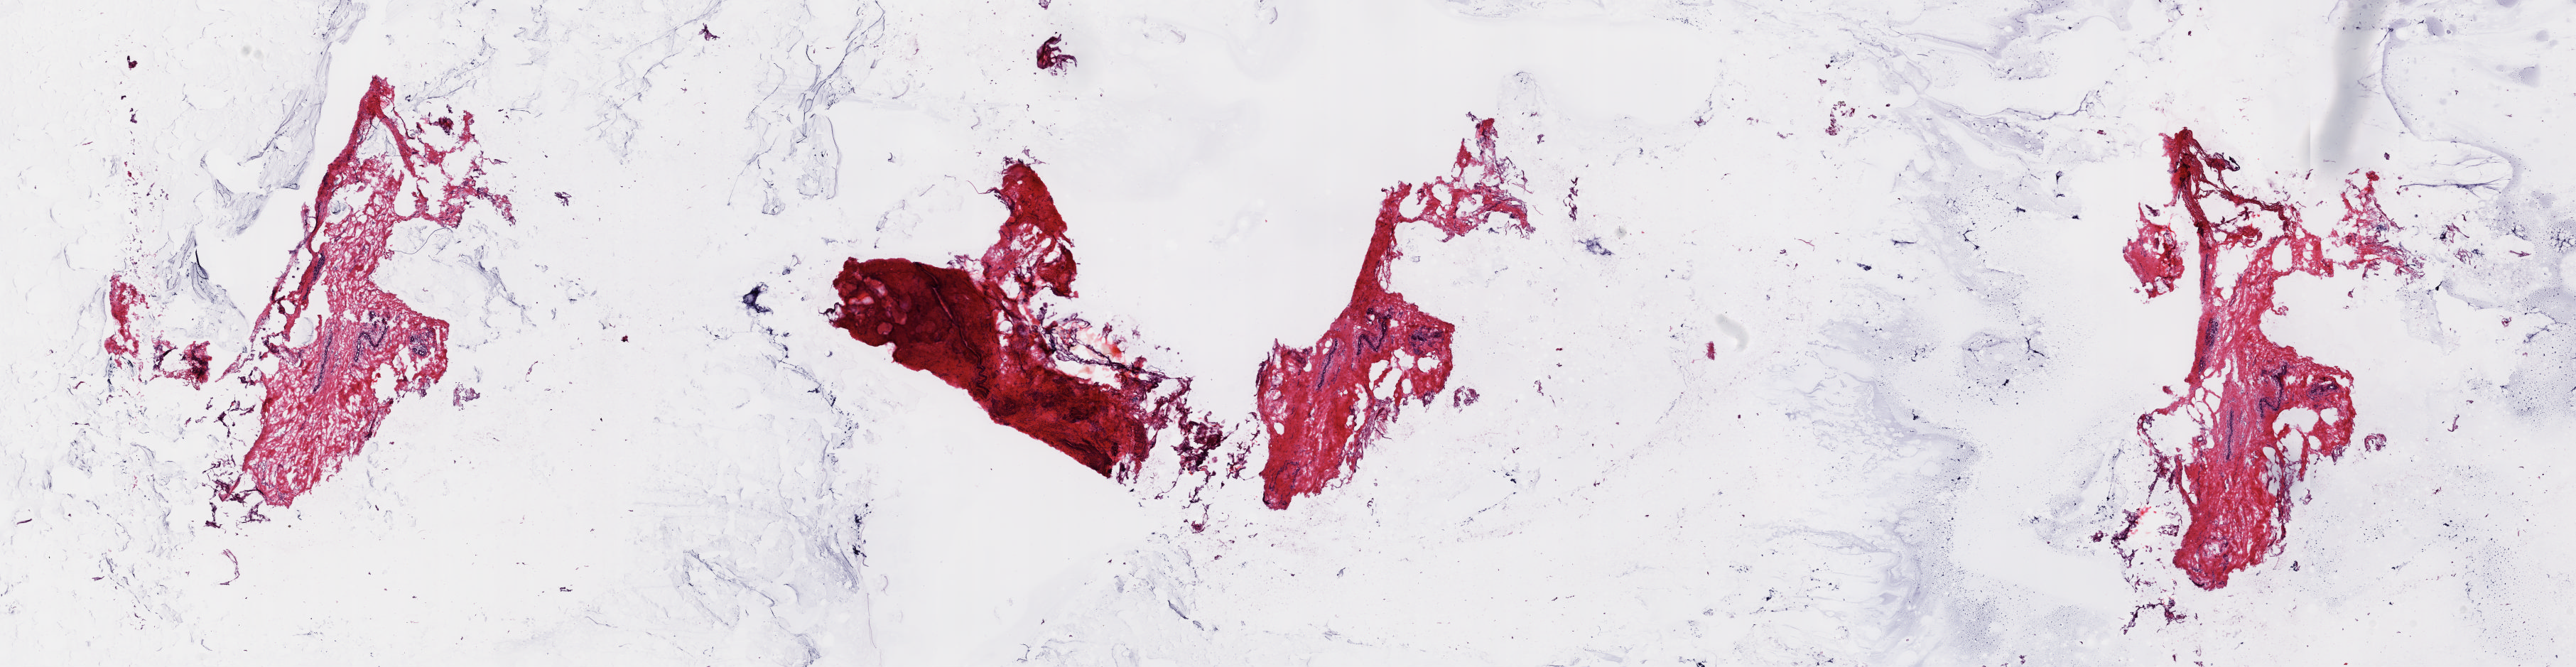
Digitized Hematoxylin and eosin (H&E) stained tissue section (whole slide), low-resolution overview of the scanned area, about 28.8 x 7.4 mm; frozen section from the top of the tissue portion; breast, solid tissue normal (non-tumour tissue) sample. Female, age 44 years at initial diagnosis. Slide review estimates, as recorded: tumour cells 0%, tumour nuclei 0%, normal cells 100%, stromal cells 0%, necrosis 0%. Inflammatory infiltration, as recorded: lymphocyte infiltration 0%, monocyte infiltration 0%, neutrophil infiltration 0%.
• this section: solid tissue normal sample (biorepository sample class)
• patient diagnosis: Infiltrating duct carcinoma, NOS